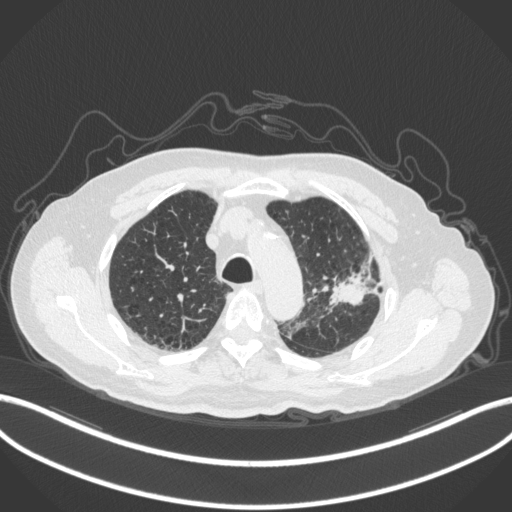
Chest CT, one axial slice; slice 228 of 331 in the series (ordered by position); 120 kVp; lung window (W 1500 / L -600 HU); 512 × 512 image matrix, field of view 400 × 400 mm. Patient: male, 79 years. From the clinical record (not read from this slice): clinical TNM (as recorded): T2a N1 M1; histopathological grade: G3.
Outlined on this slice (bounding box drawn by a radiologist):
- lung tumour (recorded histology: adenocarcinoma): box from (x=323, y=257) to (x=385, y=307) px